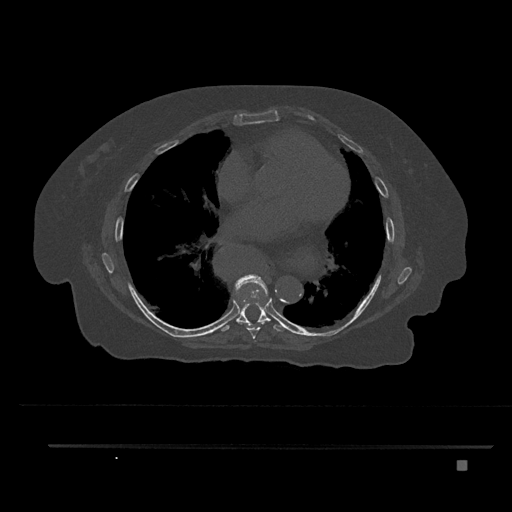
CT including the spine, one axial slice; position 463 of 797 along the scan axis; reconstruction kernel Br40s/3; bone window (W 1800 / L 400 HU); 0.5 mm slice thickness; 512 × 512 image matrix. Patient: female, 76 years. From the clinical record (not read from this slice): primary cancer: lung; vertebrae with lytic lesions (as recorded): T11, L3.
Outlined on this slice (semi-automatically segmented with operator editing):
- T7 vertebra: bounding box [x1, y1, x2, y2] px = [235, 274, 268, 339]
- T8 vertebra: [221, 302, 289, 332]